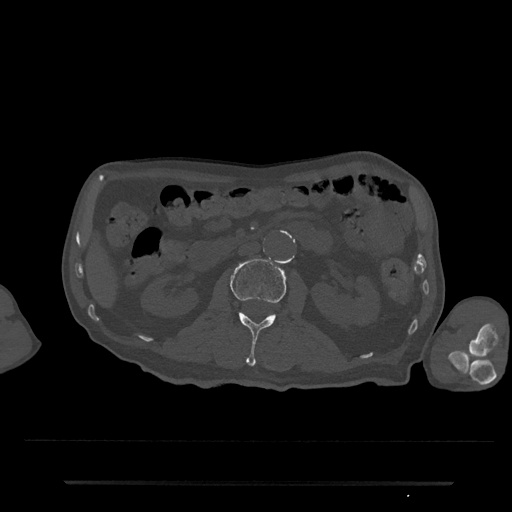
CT including the spine, one axial slice; slice 50 of 797 in the series (ordered by position); bone window (W 1800 / L 400 HU); 0.5 mm slice thickness; 512 × 512 image matrix, field of view 427 × 427 mm. Patient: male, 74 years. From the clinical record (not read from this slice): primary cancer: prostate.
Annotated regions visible in this slice (semi-automatic segmentation, software-assisted and operator-edited):
- L2 vertebra: bounding box [x1, y1, x2, y2] px = [231, 258, 286, 367]